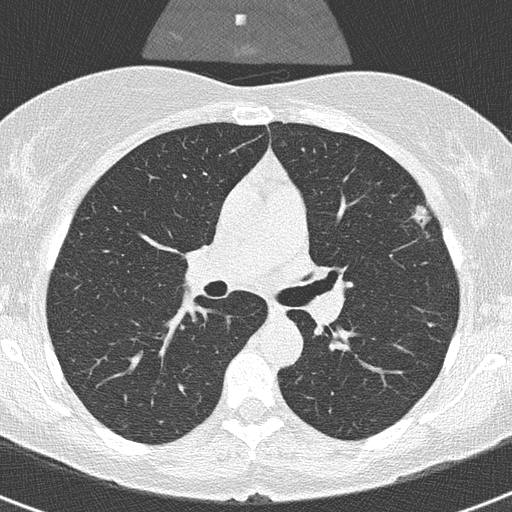
Chest CT (low-dose screening protocol), one axial image; second screening round (one year after baseline); lung window (W 1500 / L -600 HU); 512 × 512 image matrix, field of view 290 × 290 mm. Female participant, aged 56 years at enrolment.
Expert reader's lesion annotation, bounding box (x1, y1, x2, y2) in pixels: (407, 201, 455, 254). Reader record for this screening exam (exam-level; its link to the box is not recorded): non-calcified nodule or mass ≥4 mm, left upper lobe, 20 × 9 mm, smooth margins, soft tissue attenuation, pre-existing on the prior screen: yes; interval growth: yes. Later outcome: lung cancer diagnosed 55 days after this screen — adenocarcinoma, NOS, left upper lobe, moderately differentiated (G2), stage IA (AJCC 6th edition), 11 mm at pathology.